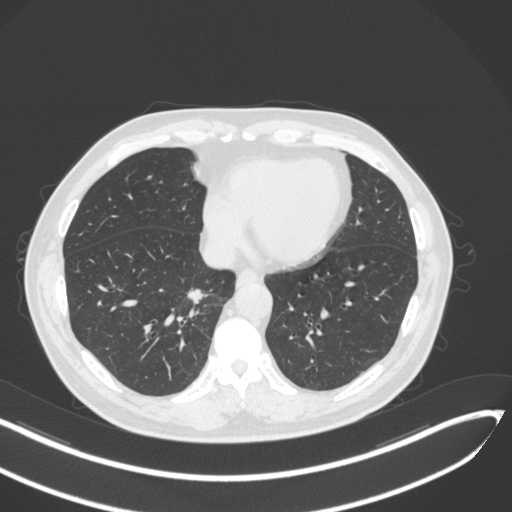
Chest CT, one axial slice; slice 123 of 429 in the series (ordered by position); reconstruction kernel B31f; 120 kVp; lung window (W 1500 / L -600 HU); 512 × 512 image matrix, field of view 400 × 400 mm. Male patient, age 62 years. From the clinical record (not read from this slice): clinical TNM (as recorded): T1b N0 M0.
Structures marked on this image (rectangle marked by the reading radiologist):
- lung tumour (recorded histology: adenocarcinoma): box from (x=180, y=285) to (x=208, y=307) px